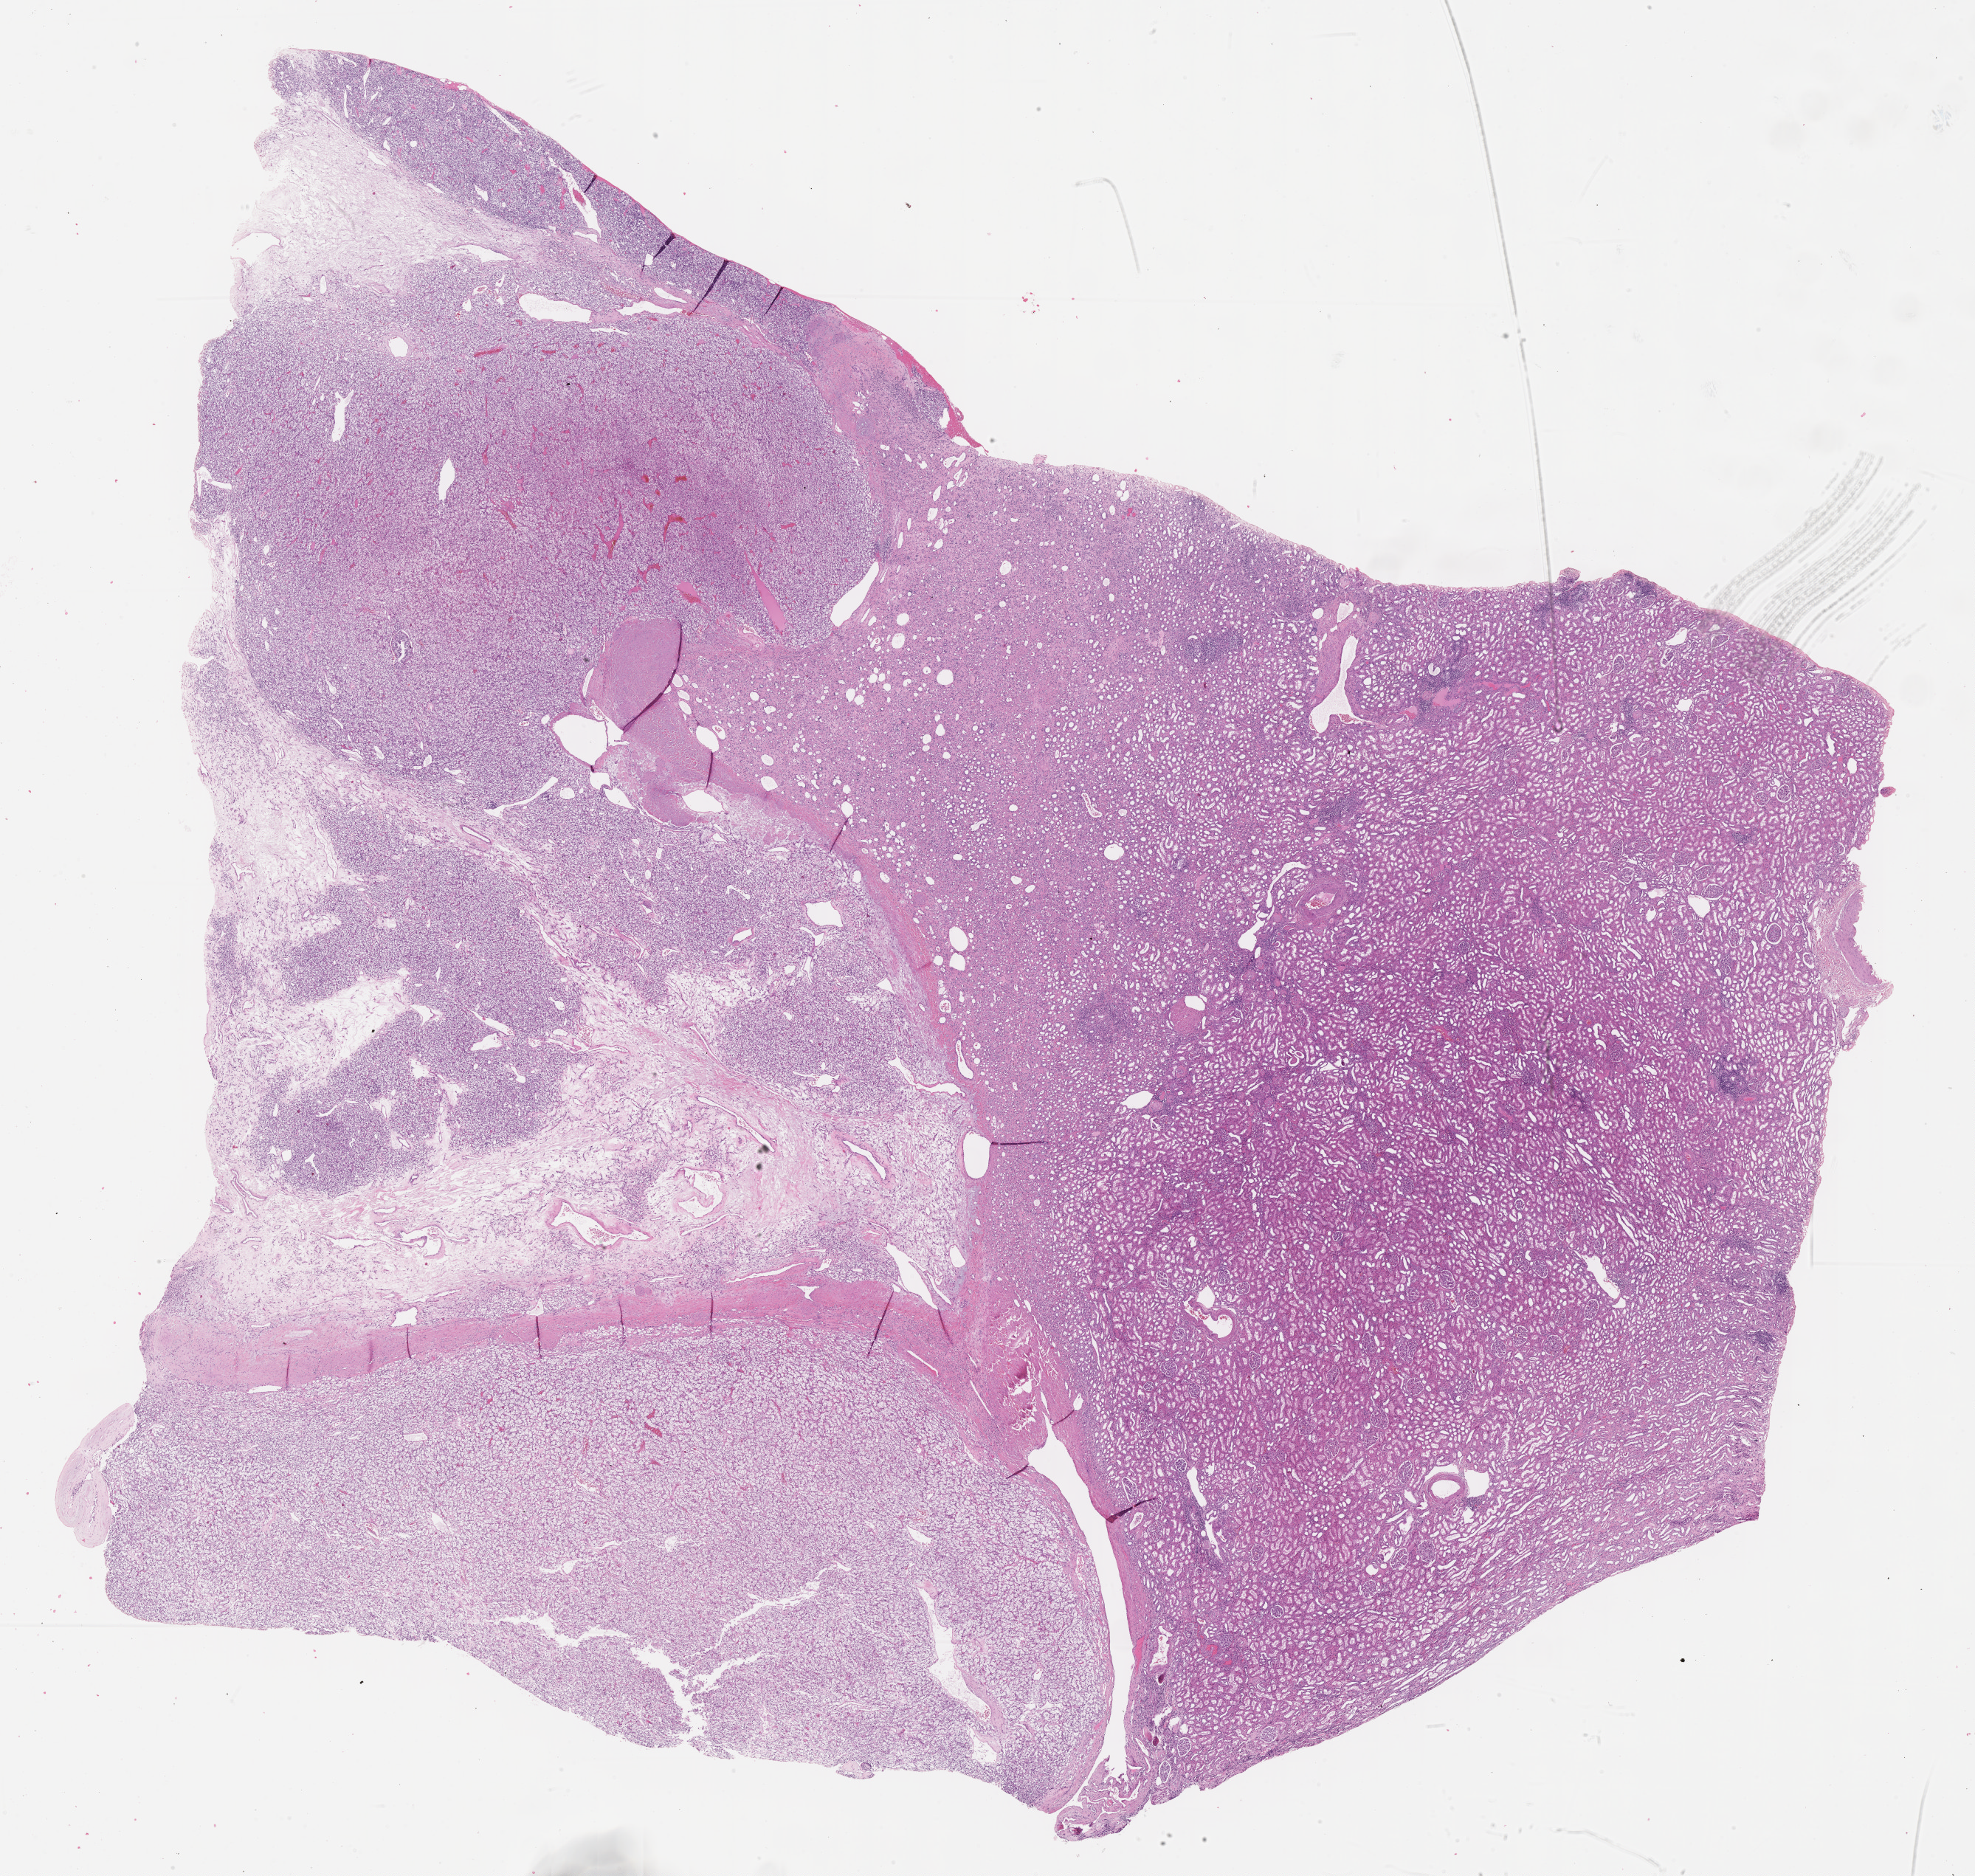
Digitized H&E-stained tissue section (whole slide), a low-resolution overview of the entire scanned area, about 21.6 x 20.6 mm (acquisition: 40x scan); formalin-fixed paraffin-embedded (FFPE) diagnostic section; sample: primary tumour, kidney. Female patient; age at initial diagnosis 67 years. Histologic grade: G3 (poorly differentiated).
AJCC pathologic stage: II. Diagnosis: Clear cell adenocarcinoma, NOS. TNM: T2b N0 M0.